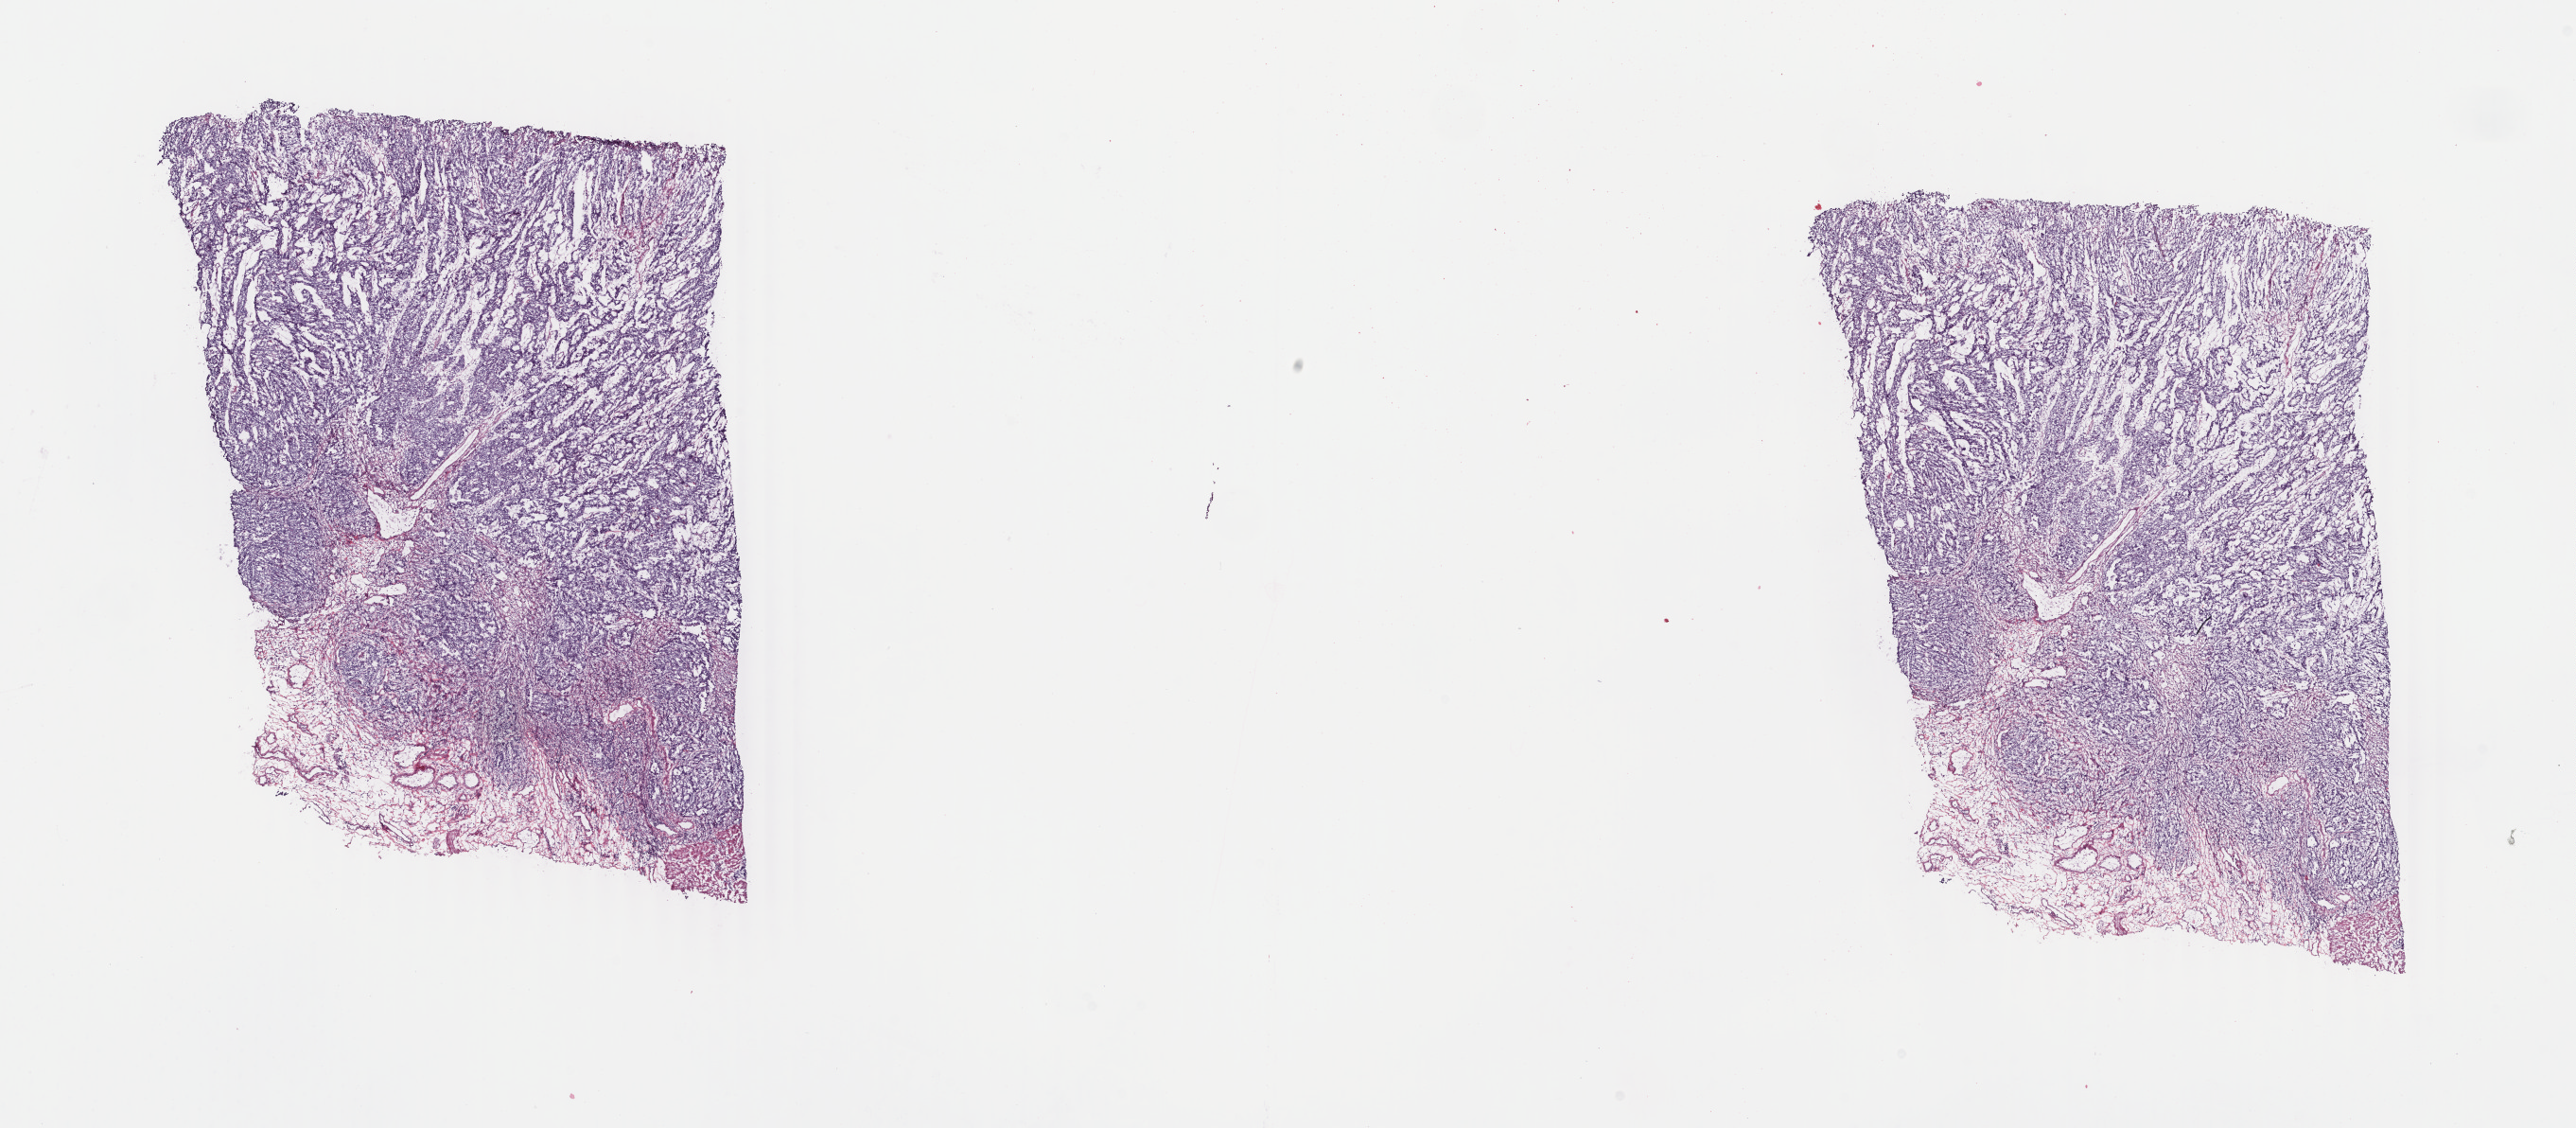
Whole-slide histology image, H&E — a low-resolution overview of the entire scanned area, about 21.7 x 9.5 mm (slide scanned at 40x); frozen section from the top of the tissue portion; stomach, primary tumour sample. Male, age 63 years at initial diagnosis. Histologic grade: G3 (poorly differentiated). Slide review estimates, as recorded: tumour cells 90%, tumour nuclei 75%, normal cells 10%, stromal cells 0%, necrosis 0%. Infiltration values recorded for this section: lymphocyte infiltration 5%, monocyte infiltration 0%, neutrophil infiltration 1%.
Lymph nodes positive (case pathology): 1 of 5 examined. Pathologic diagnosis: Adenocarcinoma, NOS (gastric antrum). AJCC pathologic stage: IIIA (7th edition). TNM: T4a N1 M0.